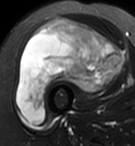
MRI of an extremity soft-tissue mass, one axial slice. Position 51 of 95 along the scan axis. T2-weighted fat-saturated. MR volume resampled by the dataset authors to the PET/CT grid (not the native acquisition matrix). 3.27 mm slice thickness. 135 × 146 image matrix, field of view 132 × 143 mm. Female patient. Case-level facts recorded for this patient, not image findings: histological type: pleiomorphic undifferentiated sarcoma; grade: high; site of the primary tumour: right quadricep.
Structures marked on this image (expert contour drawn on MRI and transferred to this co-registered scan by the dataset authors):
- gross tumour volume including surrounding oedema: box from (x=16, y=18) to (x=125, y=124) px
- gross tumour volume (mass): (x=16, y=18)–(x=125, y=124)